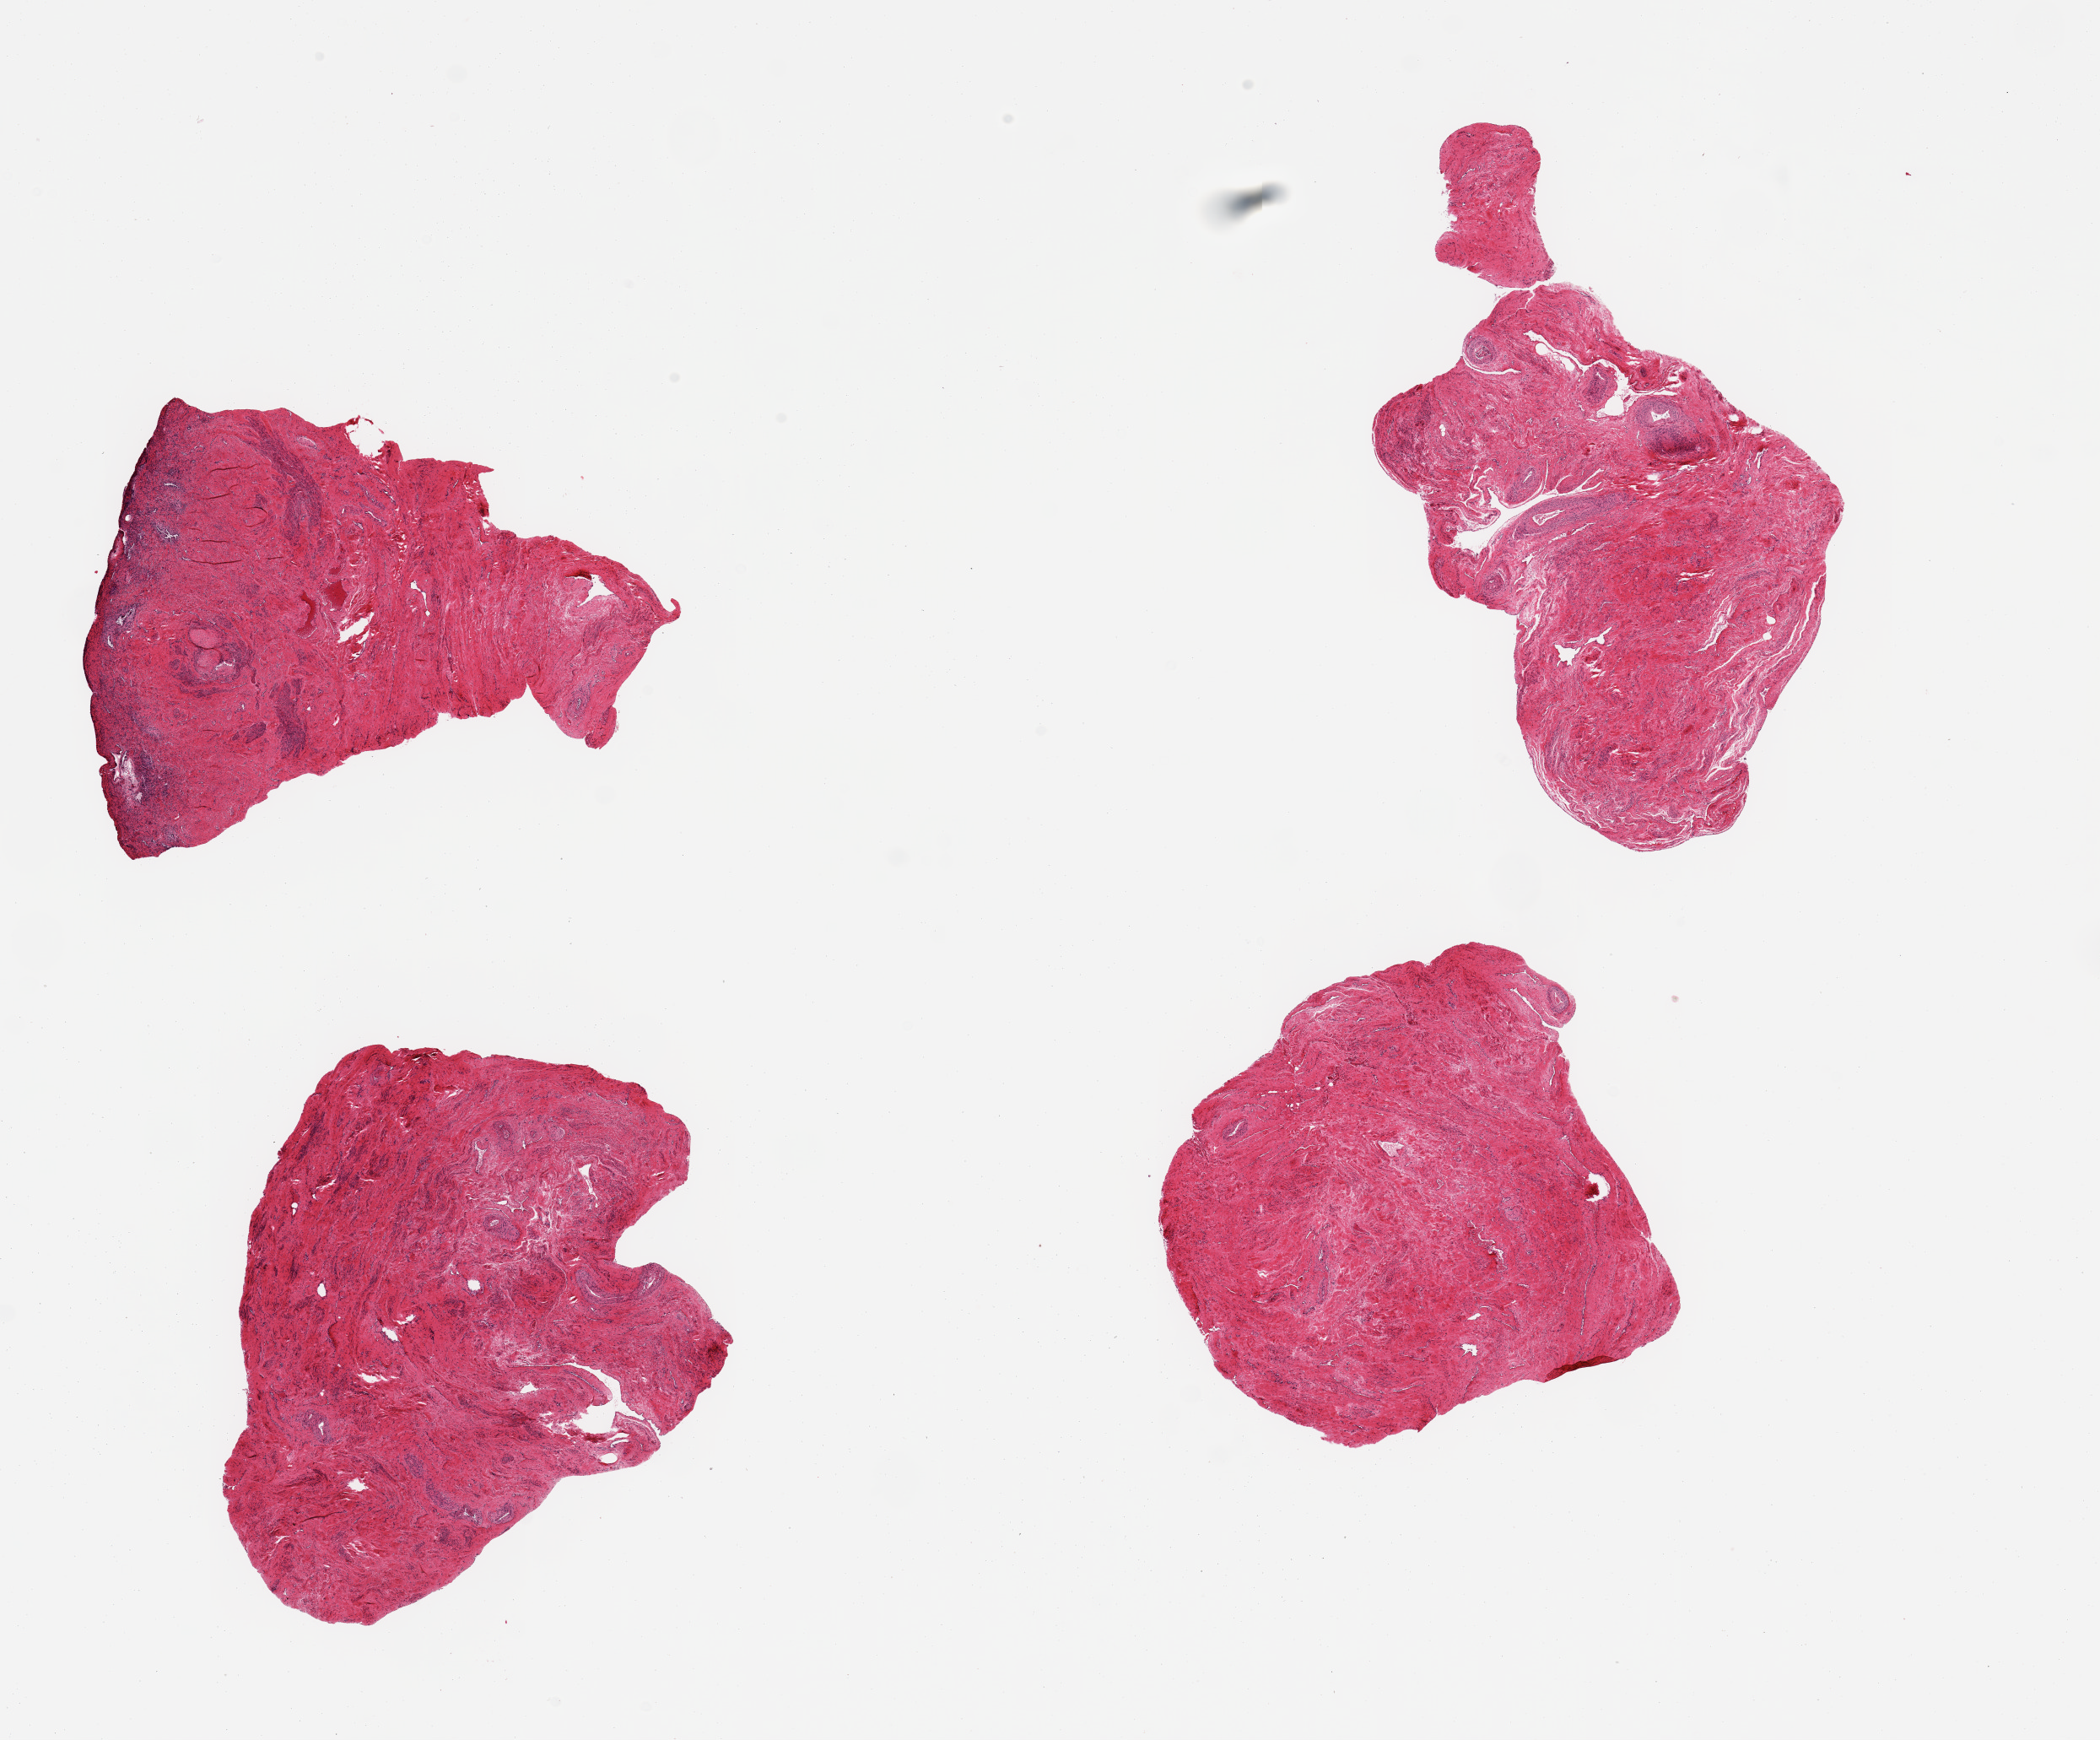
Hematoxylin and eosin (H&E) whole-slide image — whole scanned area (about 19.7 x 16.3 mm, slide scanned at 20x) shown as a low-resolution overview, PAXgene-fixed paraffin-embedded (PFPE) section, sampled site (target tissue): endocervix, donor tissue sample. Female donor.
* pathologist's review note for this sample: 4 pieces, ~5x4mm. Only one aliquot has minute endocervical glands